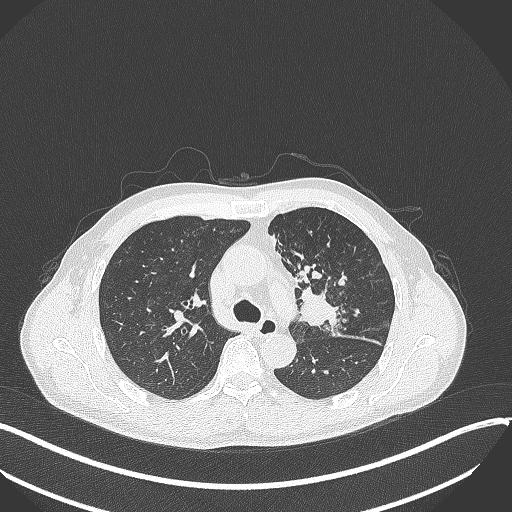
Chest CT, one axial slice; slice 228 of 411 in the series (ordered by position); reconstruction kernel B70f; lung window (W 1500 / L -600 HU); 1 mm slice thickness; 512 × 512 image matrix, field of view 400 × 400 mm. Male patient, age 56 years. From the clinical record (not read from this slice): clinical TNM (as recorded): T2a N0 M0.
Structures marked on this image (bounding box drawn by a radiologist):
- lung tumour (recorded histology: squamous cell carcinoma): bounding box (x1, y1, x2, y2) in pixels: (296, 282, 347, 336)